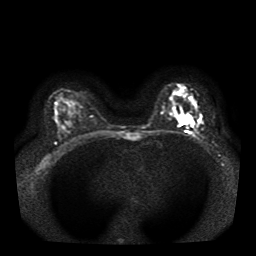
Breast MRI, one axial slice. Slice 25 of 41 in the series (ordered by position). Diffusion-weighted series; image 2 of 4 stored at this slice position (different b-values; order by instance number). 1.5 T. 5 mm slice thickness. 256 × 256 image matrix. Female patient.
Annotated regions visible in this slice (expert manual segmentation):
- tumour on diffusion-weighted imaging: bounding box (x1, y1, x2, y2) in pixels: (179, 114, 194, 126)